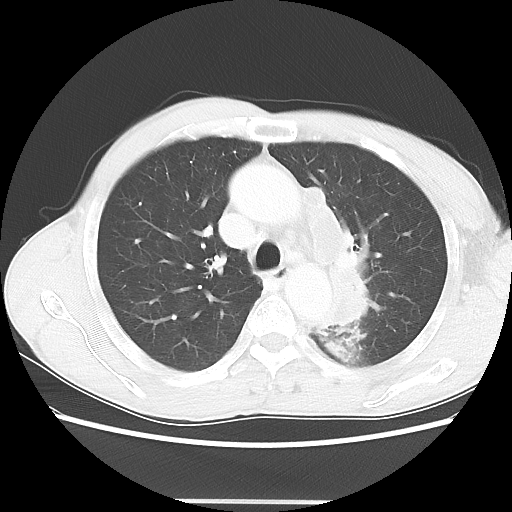
Chest CT, one axial slice; slice 45 of 62 in the series (ordered by position); reconstruction kernel LUNG; 100 kVp; lung window (W 1500 / L -600 HU); 5 mm slice thickness; 512 × 512 image matrix, field of view 360 × 360 mm. Patient: male, 61 years. Case-level facts recorded for this patient, not image findings: clinical TNM (as recorded): T3 N1 M1.
Annotated regions visible in this slice (bounding box drawn by a radiologist):
- lung tumour (recorded histology: adenocarcinoma): bounding box (x1, y1, x2, y2) in pixels: (304, 181, 378, 339)